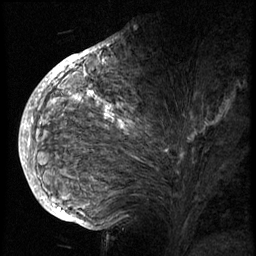
Breast MRI (dynamic contrast-enhanced), one sagittal slice. Position 38 of 74 along the scan axis. 3 images stored at this slice position (order not interpretable as contrast timing). 1.5 T. TE 4.2 ms, TR 8.9 ms. 256 × 256 image matrix, field of view 200 × 200 mm. Female patient, age 57 years. Case-level facts recorded for this patient, not image findings: setting: breast cancer imaged before/during neoadjuvant chemotherapy; receptor status: HER2-positive.
Outlined on this slice (semi-automatic segmentation, software-assisted and operator-edited):
- analysis volume of interest (the breast-tissue region the enhancement analysis was run in; not a lesion): bounding box (x1, y1, x2, y2) in pixels: (40, 62, 241, 175)
- tumour enhancement mask (voxels above the 140 % enhancement threshold inside the analysis volume of interest): (53, 62, 183, 157)